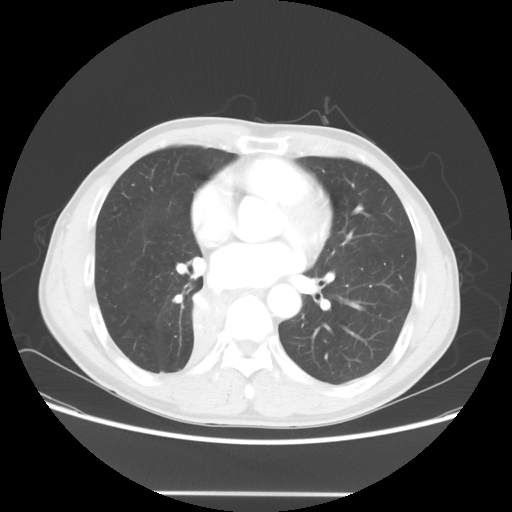
Chest CT, one axial slice; position 28 of 62 along the scan axis; reconstruction kernel STANDARD; 120 kVp; lung window (W 1500 / L -600 HU); 5 mm slice thickness; 512 × 512 image matrix. Patient: male, 47 years. From the clinical record (not read from this slice): clinical TNM (as recorded): T2 N0 M0; histopathological grade: G2.
Structures marked on this image (bounding box drawn by a radiologist):
- lung tumour (recorded histology: squamous cell carcinoma): bounding box (x1, y1, x2, y2) in pixels: (177, 275, 220, 361)